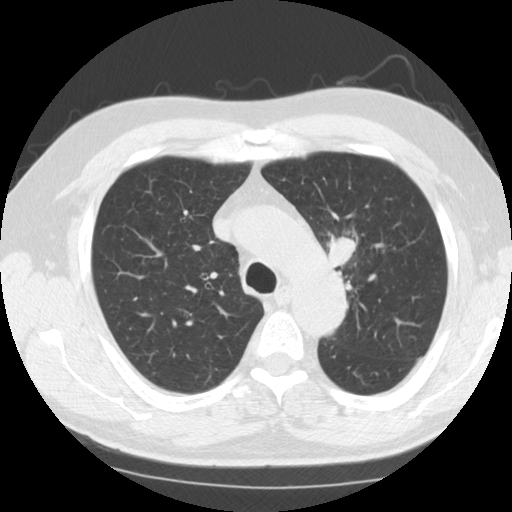
Low-dose screening chest CT, one axial slice. Slice 93 of 124 in the series (ordered by position). 120 kVp. Lung window (W 1500 / L -600 HU). 2.5 mm slice thickness. 512 × 512 image matrix.
Annotated regions visible in this slice (expert manual segmentation):
- lesion 1 (tumor, upper lobe of left lung): bounding box [x1, y1, x2, y2] px = [327, 235, 357, 266]